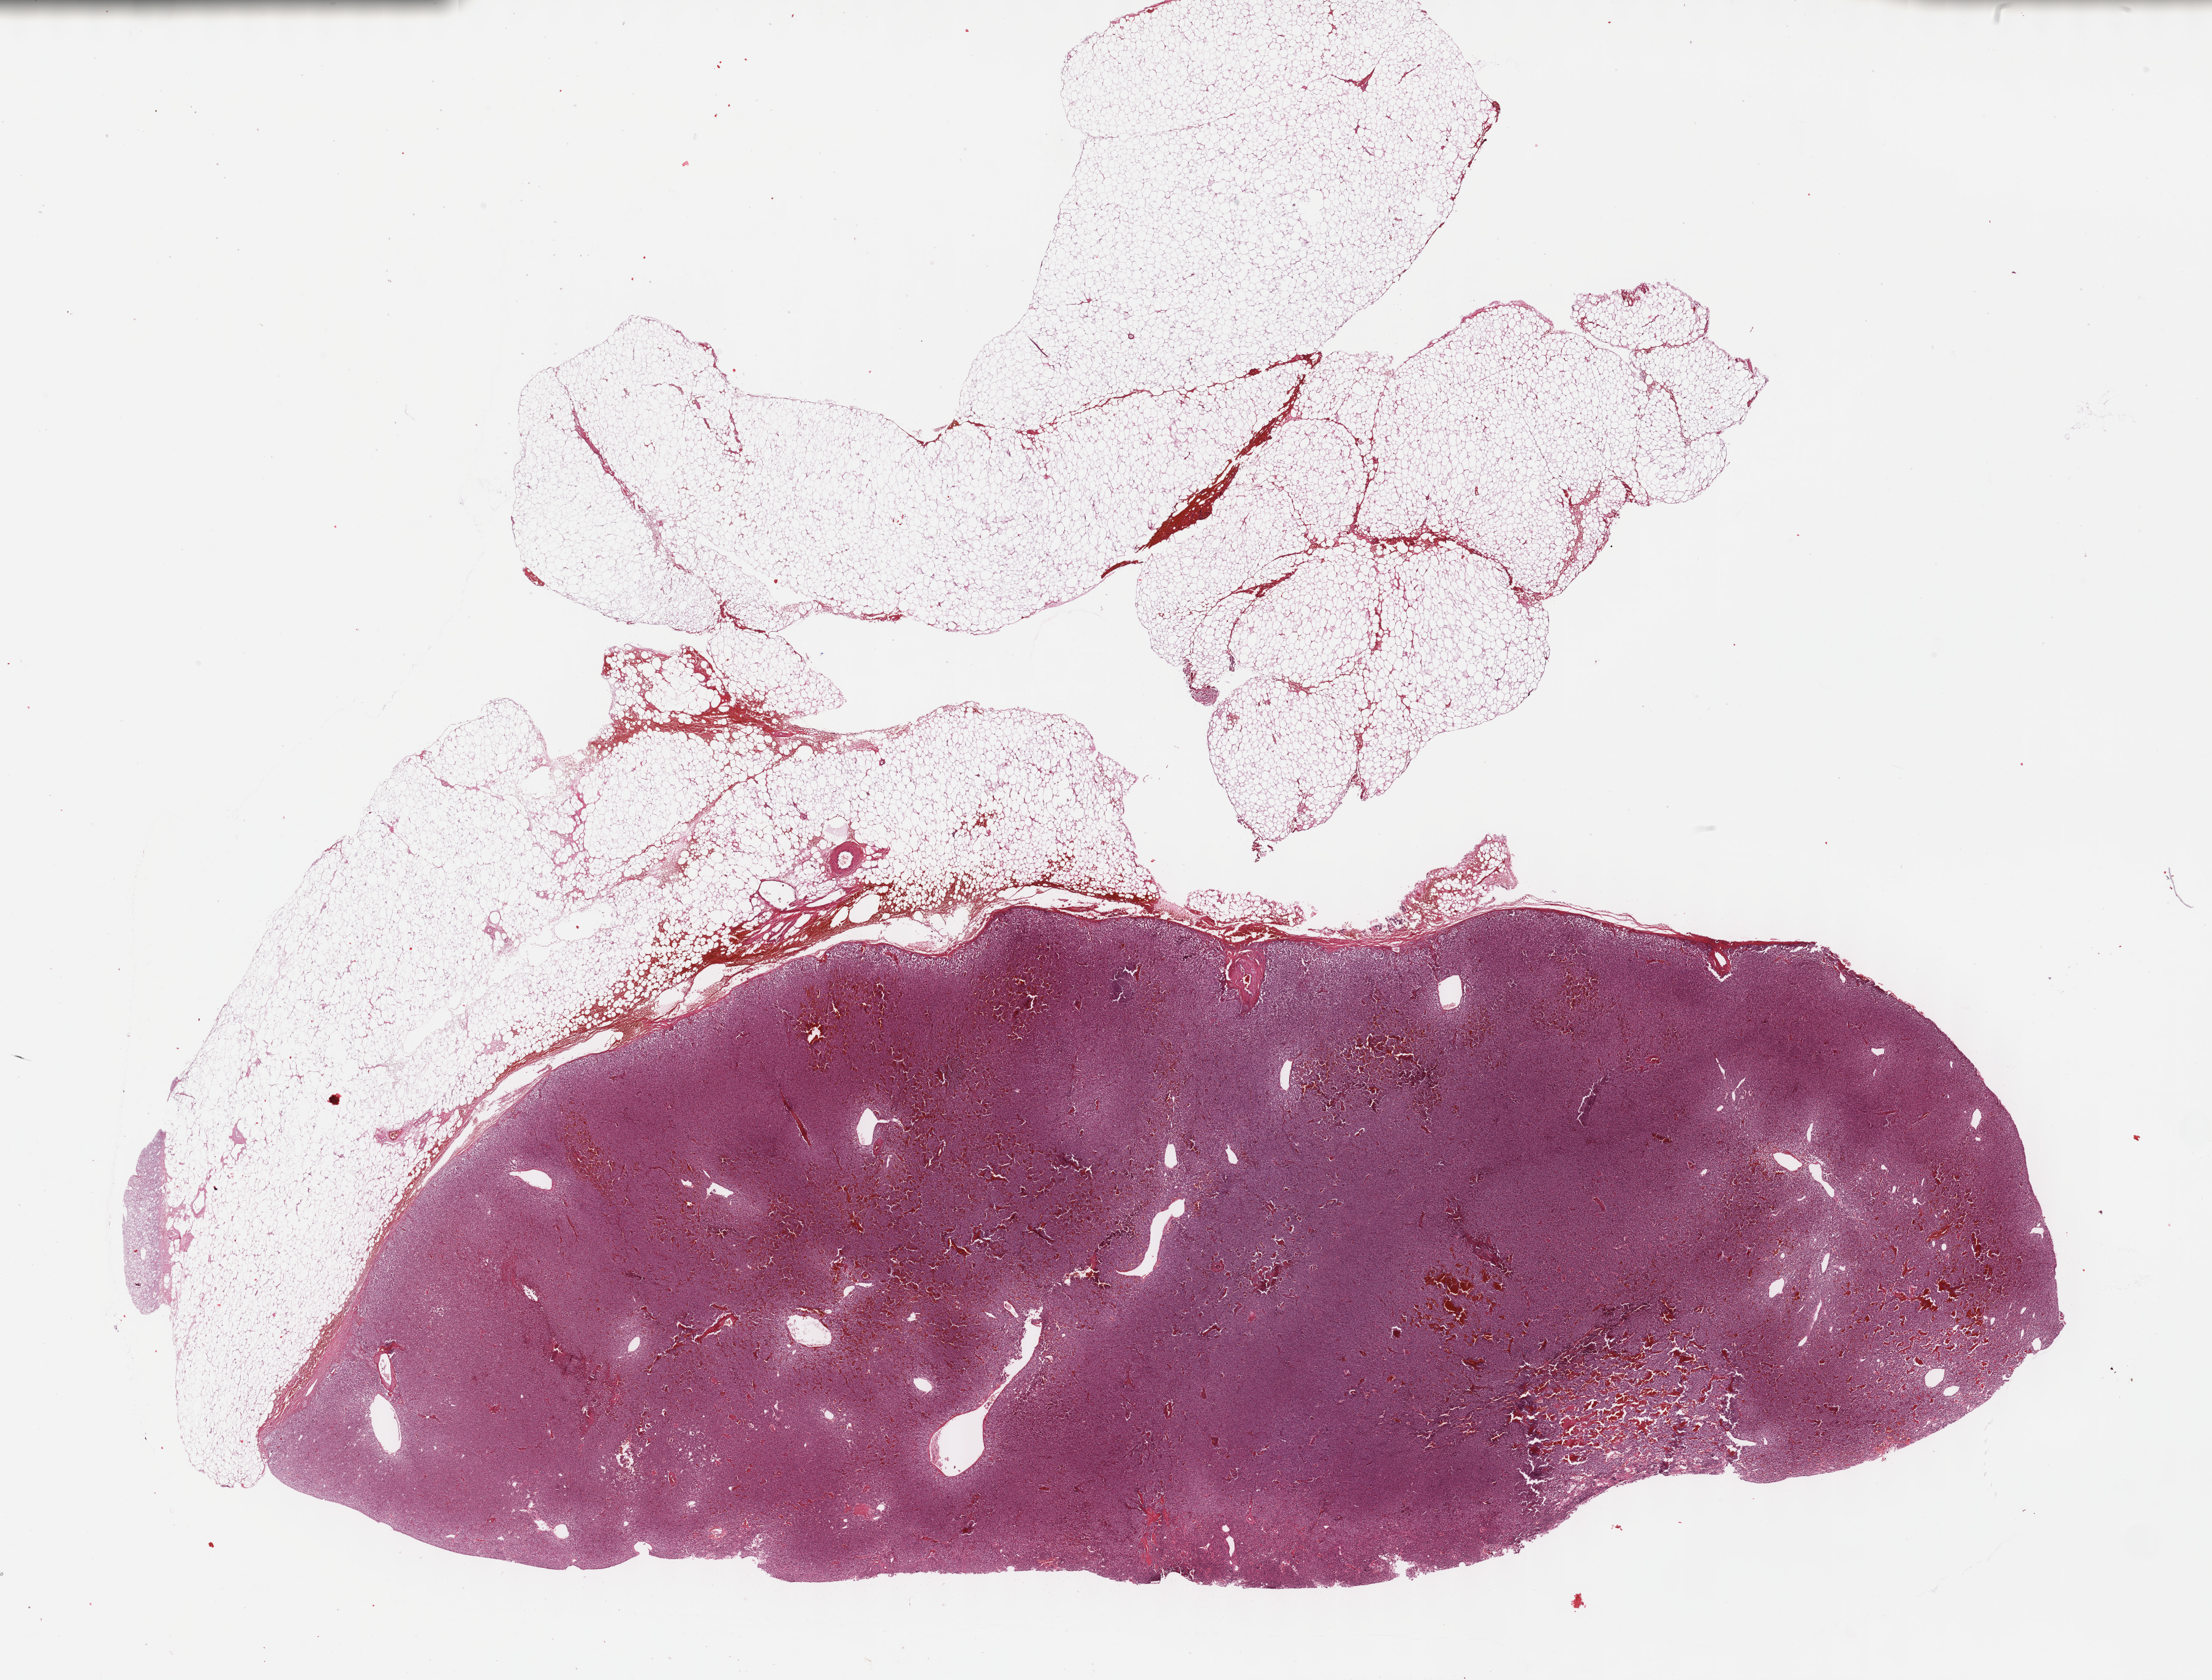
H&E-stained whole-slide image — low-resolution overview of the scanned area, about 29.2 x 22.2 mm (acquisition: 40x scan); FFPE section; primary tumour sample from the adrenal gland. Female, age 63 years at initial diagnosis.
• pathologic diagnosis: Pheochromocytoma, malignant
• laterality: left